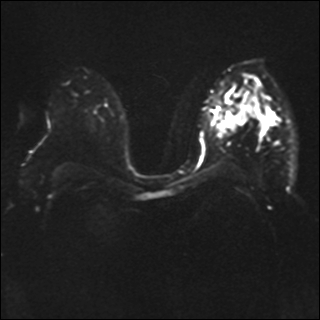
Breast MRI, one axial slice. Diffusion-weighted series; image 2 of 4 stored at this slice position (different b-values; order by instance number). 1.5 T. 320 × 320 image matrix. Female patient.
Structures marked on this image (outlined manually by an expert reader):
- tumour on diffusion-weighted imaging: bounding box [x1, y1, x2, y2] px = [222, 112, 240, 129]